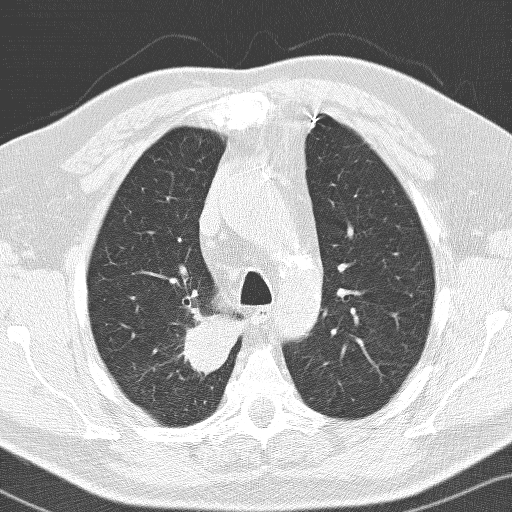
Chest CT (low-dose screening protocol), one axial image; first (baseline) screen; lung window (W 1500 / L -600 HU); lung (sharp) reconstruction kernel (D); slice 34 of 141 in the series; 512 × 512 image matrix, field of view 326 × 326 mm. Male participant, aged 66 years at enrolment. Former smoker at enrolment.
Expert-annotated lung lesion, bounding box (x1, y1, x2, y2) in pixels: (150, 304, 232, 391). Screening reader's record for this exam (one nodule recorded; not confirmed to be the boxed lesion): non-calcified nodule or mass ≥4 mm, right upper lobe, 36 × 30 mm, spiculated (stellate) margins, soft tissue attenuation. Official screen result: positive, change unspecified: nodule(s) >= 4 mm or enlarging nodule(s), mass(es), or other non-specific abnormalities suspicious for lung cancer. Later outcome: lung cancer diagnosed 103 days after this screen — adenocarcinoma, NOS, right upper lobe, poorly differentiated (G3), stage IIB (AJCC 6th edition), 33 mm at pathology.